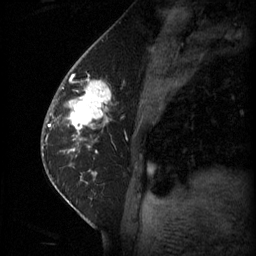
Breast MRI (dynamic contrast-enhanced), one sagittal slice; position 24 of 60 along the scan axis; 3 images stored at this slice position (order not interpretable as contrast timing); 1.5 T; TE 4.2 ms, TR 11 ms; 2 mm slice thickness; 256 × 256 image matrix, field of view 180 × 180 mm. Female patient, age 62 years.
Outlined on this slice (semi-automatically segmented with operator editing):
- analysis volume of interest (the breast-tissue region the enhancement analysis was run in; not a lesion): box from (x=55, y=72) to (x=124, y=135) px
- tumour enhancement mask (voxels above the 70 % enhancement threshold inside the analysis volume of interest): (x=63, y=82)–(x=112, y=135)